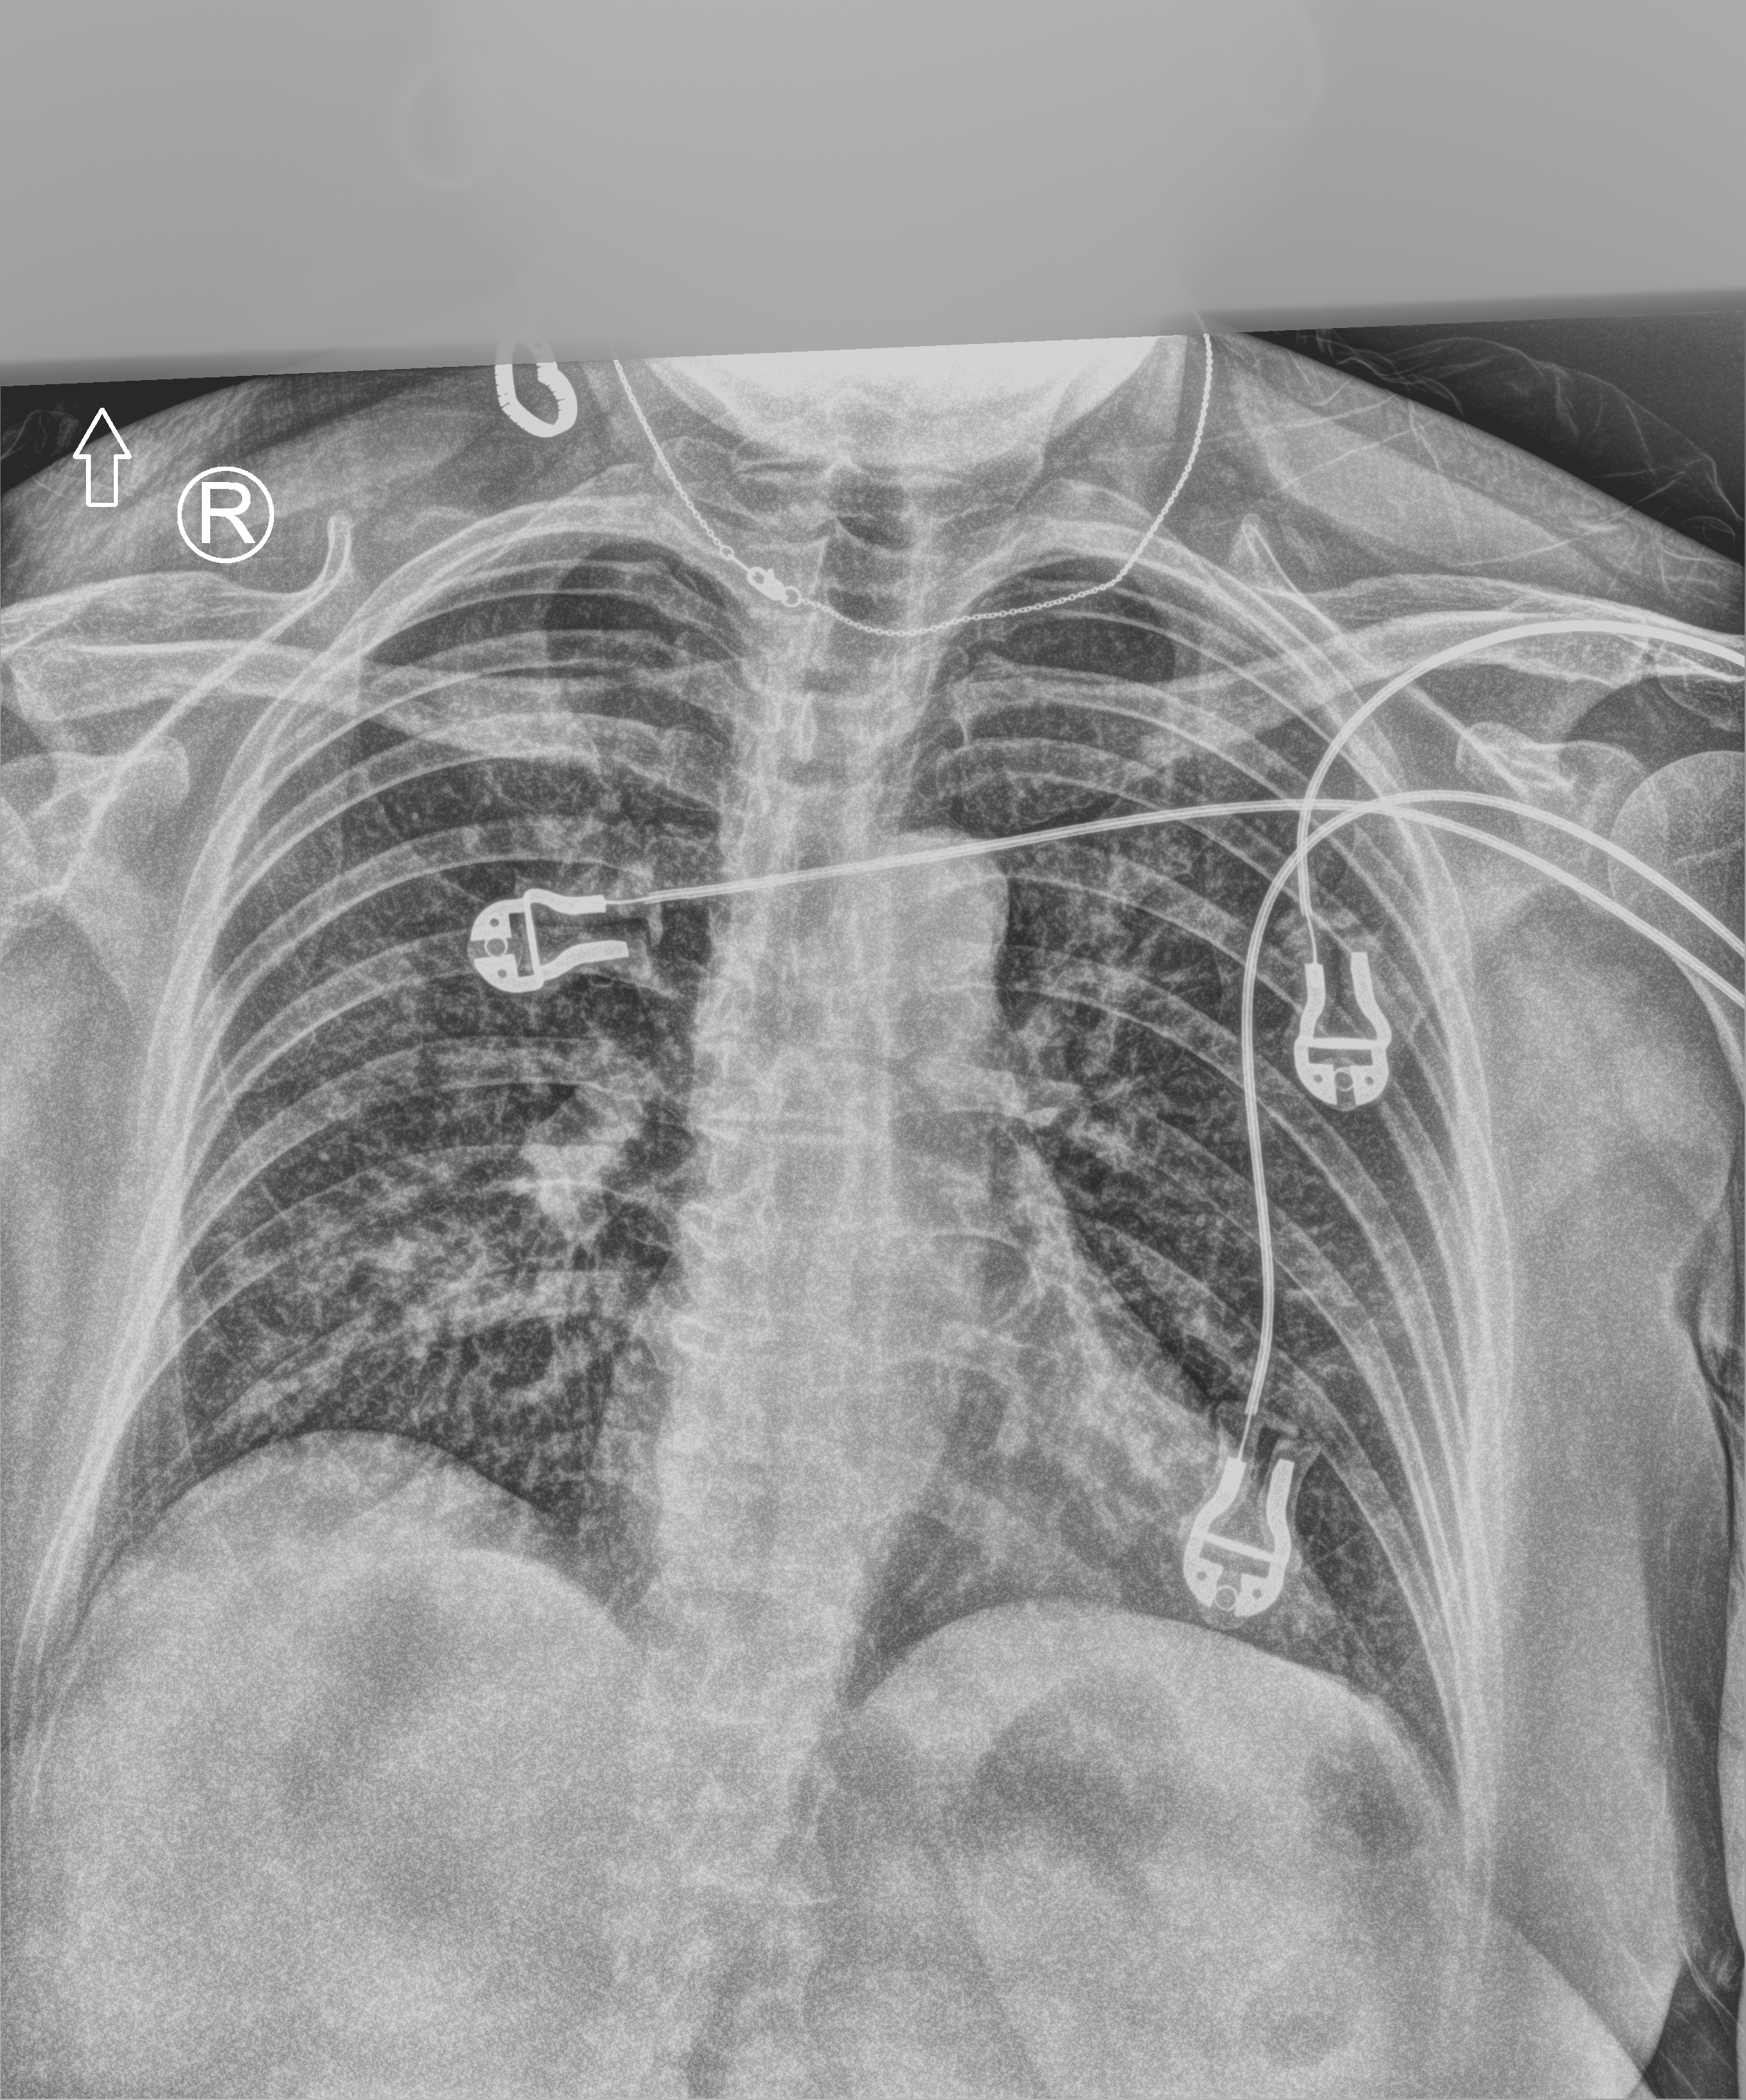
Chest X-ray (portable); anteroposterior (AP) projection. Patient hospitalised with COVID-19; female, aged 18–59 years.
Admission-level facts for this patient (not findings on this image; timing relative to this image not recorded): mechanically ventilated during this hospital stay: no; chronic kidney disease (admission record): no.